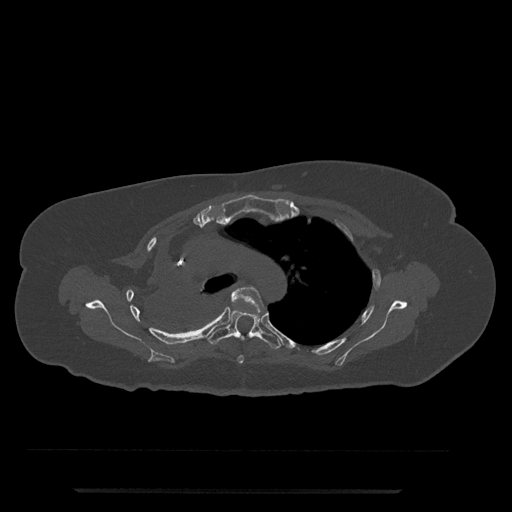
CT including the spine, one axial slice; position 560 of 797 along the scan axis; reconstruction kernel Br40s/3; 120 kVp; bone window (W 1800 / L 400 HU); 0.5 mm slice thickness; 512 × 512 image matrix, field of view 440 × 440 mm. Patient: female, 51 years. Case-level facts recorded for this patient, not image findings: primary cancer: neuro; vertebrae with lytic lesions (as recorded): T8.
Outlined on this slice (semi-automatically segmented with operator editing):
- T4 vertebra: bounding box [x1, y1, x2, y2] px = [231, 286, 264, 364]
- T5 vertebra: [206, 307, 282, 349]